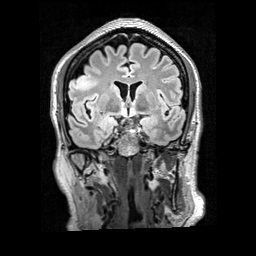
Brain MRI from a brain-tumour surgery series, one coronal slice. Position 114 of 200 along the scan axis. T2 FLAIR. 1 mm slice thickness. 256 × 256 image matrix. From the clinical record (not read from this slice): histopathology: Glioblastoma; WHO grade: 4; IDH mutation: no.
Annotated regions visible in this slice (manually delineated by an expert):
- tumour: box from (x=72, y=71) to (x=100, y=91) px